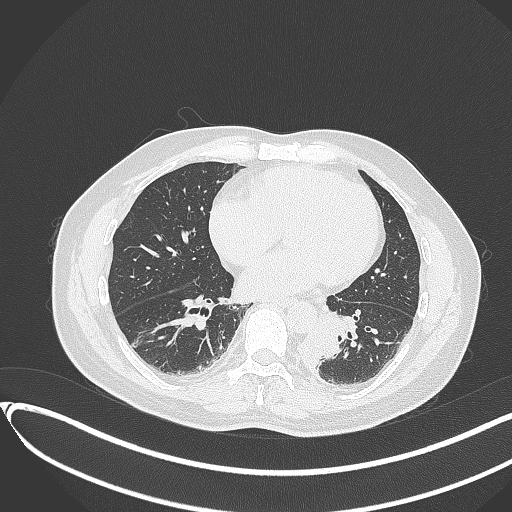
Chest CT, one axial slice. Slice 131 of 417 in the series (ordered by position). Lung window (W 1500 / L -600 HU). 1 mm slice thickness. 512 × 512 image matrix. Male patient, age 54 years. From the clinical record (not read from this slice): clinical TNM (as recorded): T3 N0 M0.
Annotated regions visible in this slice (bounding box drawn by a radiologist):
- lung tumour (recorded histology: squamous cell carcinoma): bounding box [x1, y1, x2, y2] px = [290, 307, 347, 370]